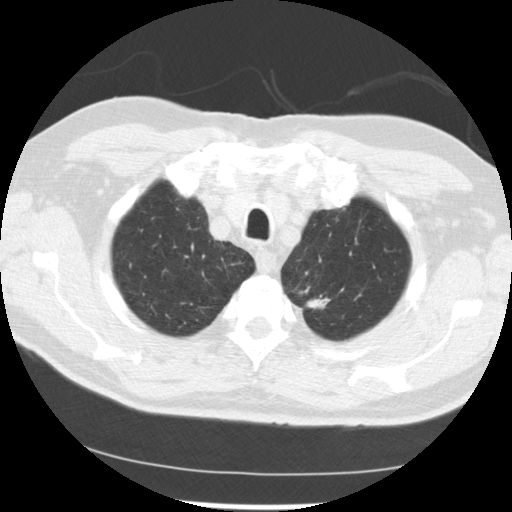
Low-dose screening chest CT, one axial slice; lung window (W 1500 / L -600 HU); 512 × 512 image matrix.
Outlined on this slice (expert manual segmentation):
- lesion 2 (tumor, upper lobe of left lung): bounding box [x1, y1, x2, y2] px = [306, 298, 329, 309]